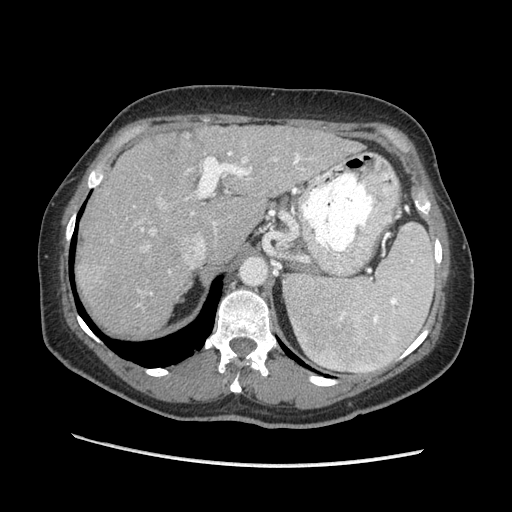
Contrast-enhanced abdominal CT (liver protocol), one axial slice. Reconstruction kernel STANDARD. Soft-tissue window (W 400 / L 40 HU). 2.5 mm slice thickness. 512 × 512 image matrix, field of view 360 × 360 mm. Case-level facts recorded for this patient, not image findings: diagnosis: hepatocellular carcinoma (patient treated with transarterial chemoembolisation; whether this scan precedes or follows treatment is not stated here); TNM stage (as recorded): Stage-II; Child-Pugh class: A; tumour nodularity: multinodular.
Outlined on this slice (semi-automatically segmented with operator editing):
- liver parenchyma outside the tumour (the mass and vessels are separate outlines, so this box may not span the whole liver): bounding box (x1, y1, x2, y2) in pixels: (76, 126, 362, 336)
- mass: (177, 129, 203, 149)
- liver vessels: (137, 152, 339, 306)